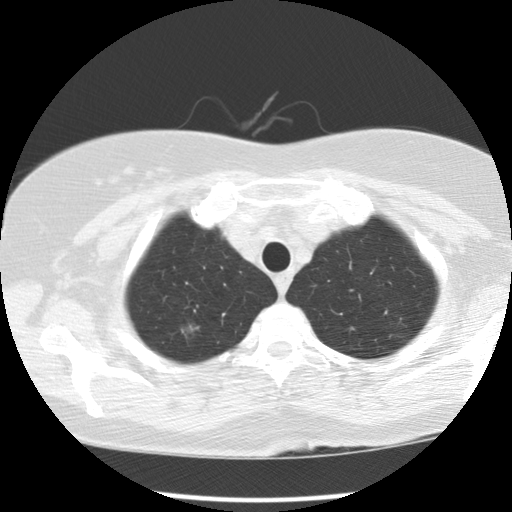
Chest CT (low-dose screening protocol), one axial image, third screening round (two years after baseline), lung window (W 1500 / L -600 HU), 120 kVp, slice 15 of 122 in the series. Female, age 72 years at enrolment. Former smoker at enrolment.
Lesion marked by an expert reader, bounding box [x1, y1, x2, y2] px = [166, 312, 208, 357]. The screening reader recorded 4 non-calcified nodules or masses ≥4 mm on this exam (right upper lobe, right upper lobe, right upper lobe, right lower lobe); which of them this box marks is not recorded. Participant outcome: lung cancer diagnosed 85 days after this screen — bronchiolo-alveolar adenocarcinoma, NOS, right upper lobe, well differentiated (G1), stage IA (AJCC 6th edition), 8 mm at pathology.